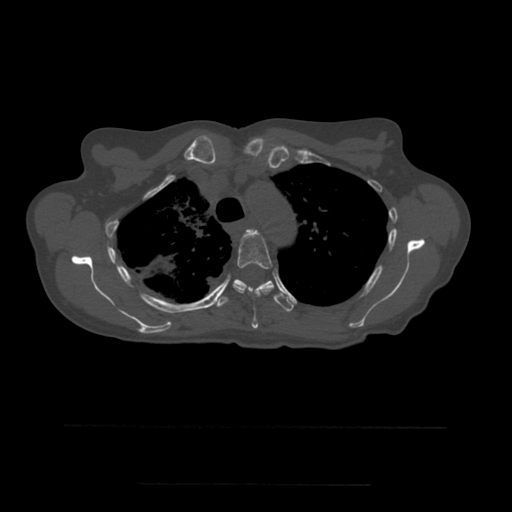
CT including the spine, one axial slice; bone window (W 1800 / L 400 HU); 512 × 512 image matrix, field of view 350 × 350 mm. Patient age 58 years. Case-level facts recorded for this patient, not image findings: primary cancer: lung.
Structures marked on this image (semi-automatically segmented with operator editing):
- T3 vertebra: bounding box (x1, y1, x2, y2) in pixels: (246, 229, 258, 234)
- T4 vertebra: (233, 232, 273, 329)
- T5 vertebra: (217, 279, 295, 312)